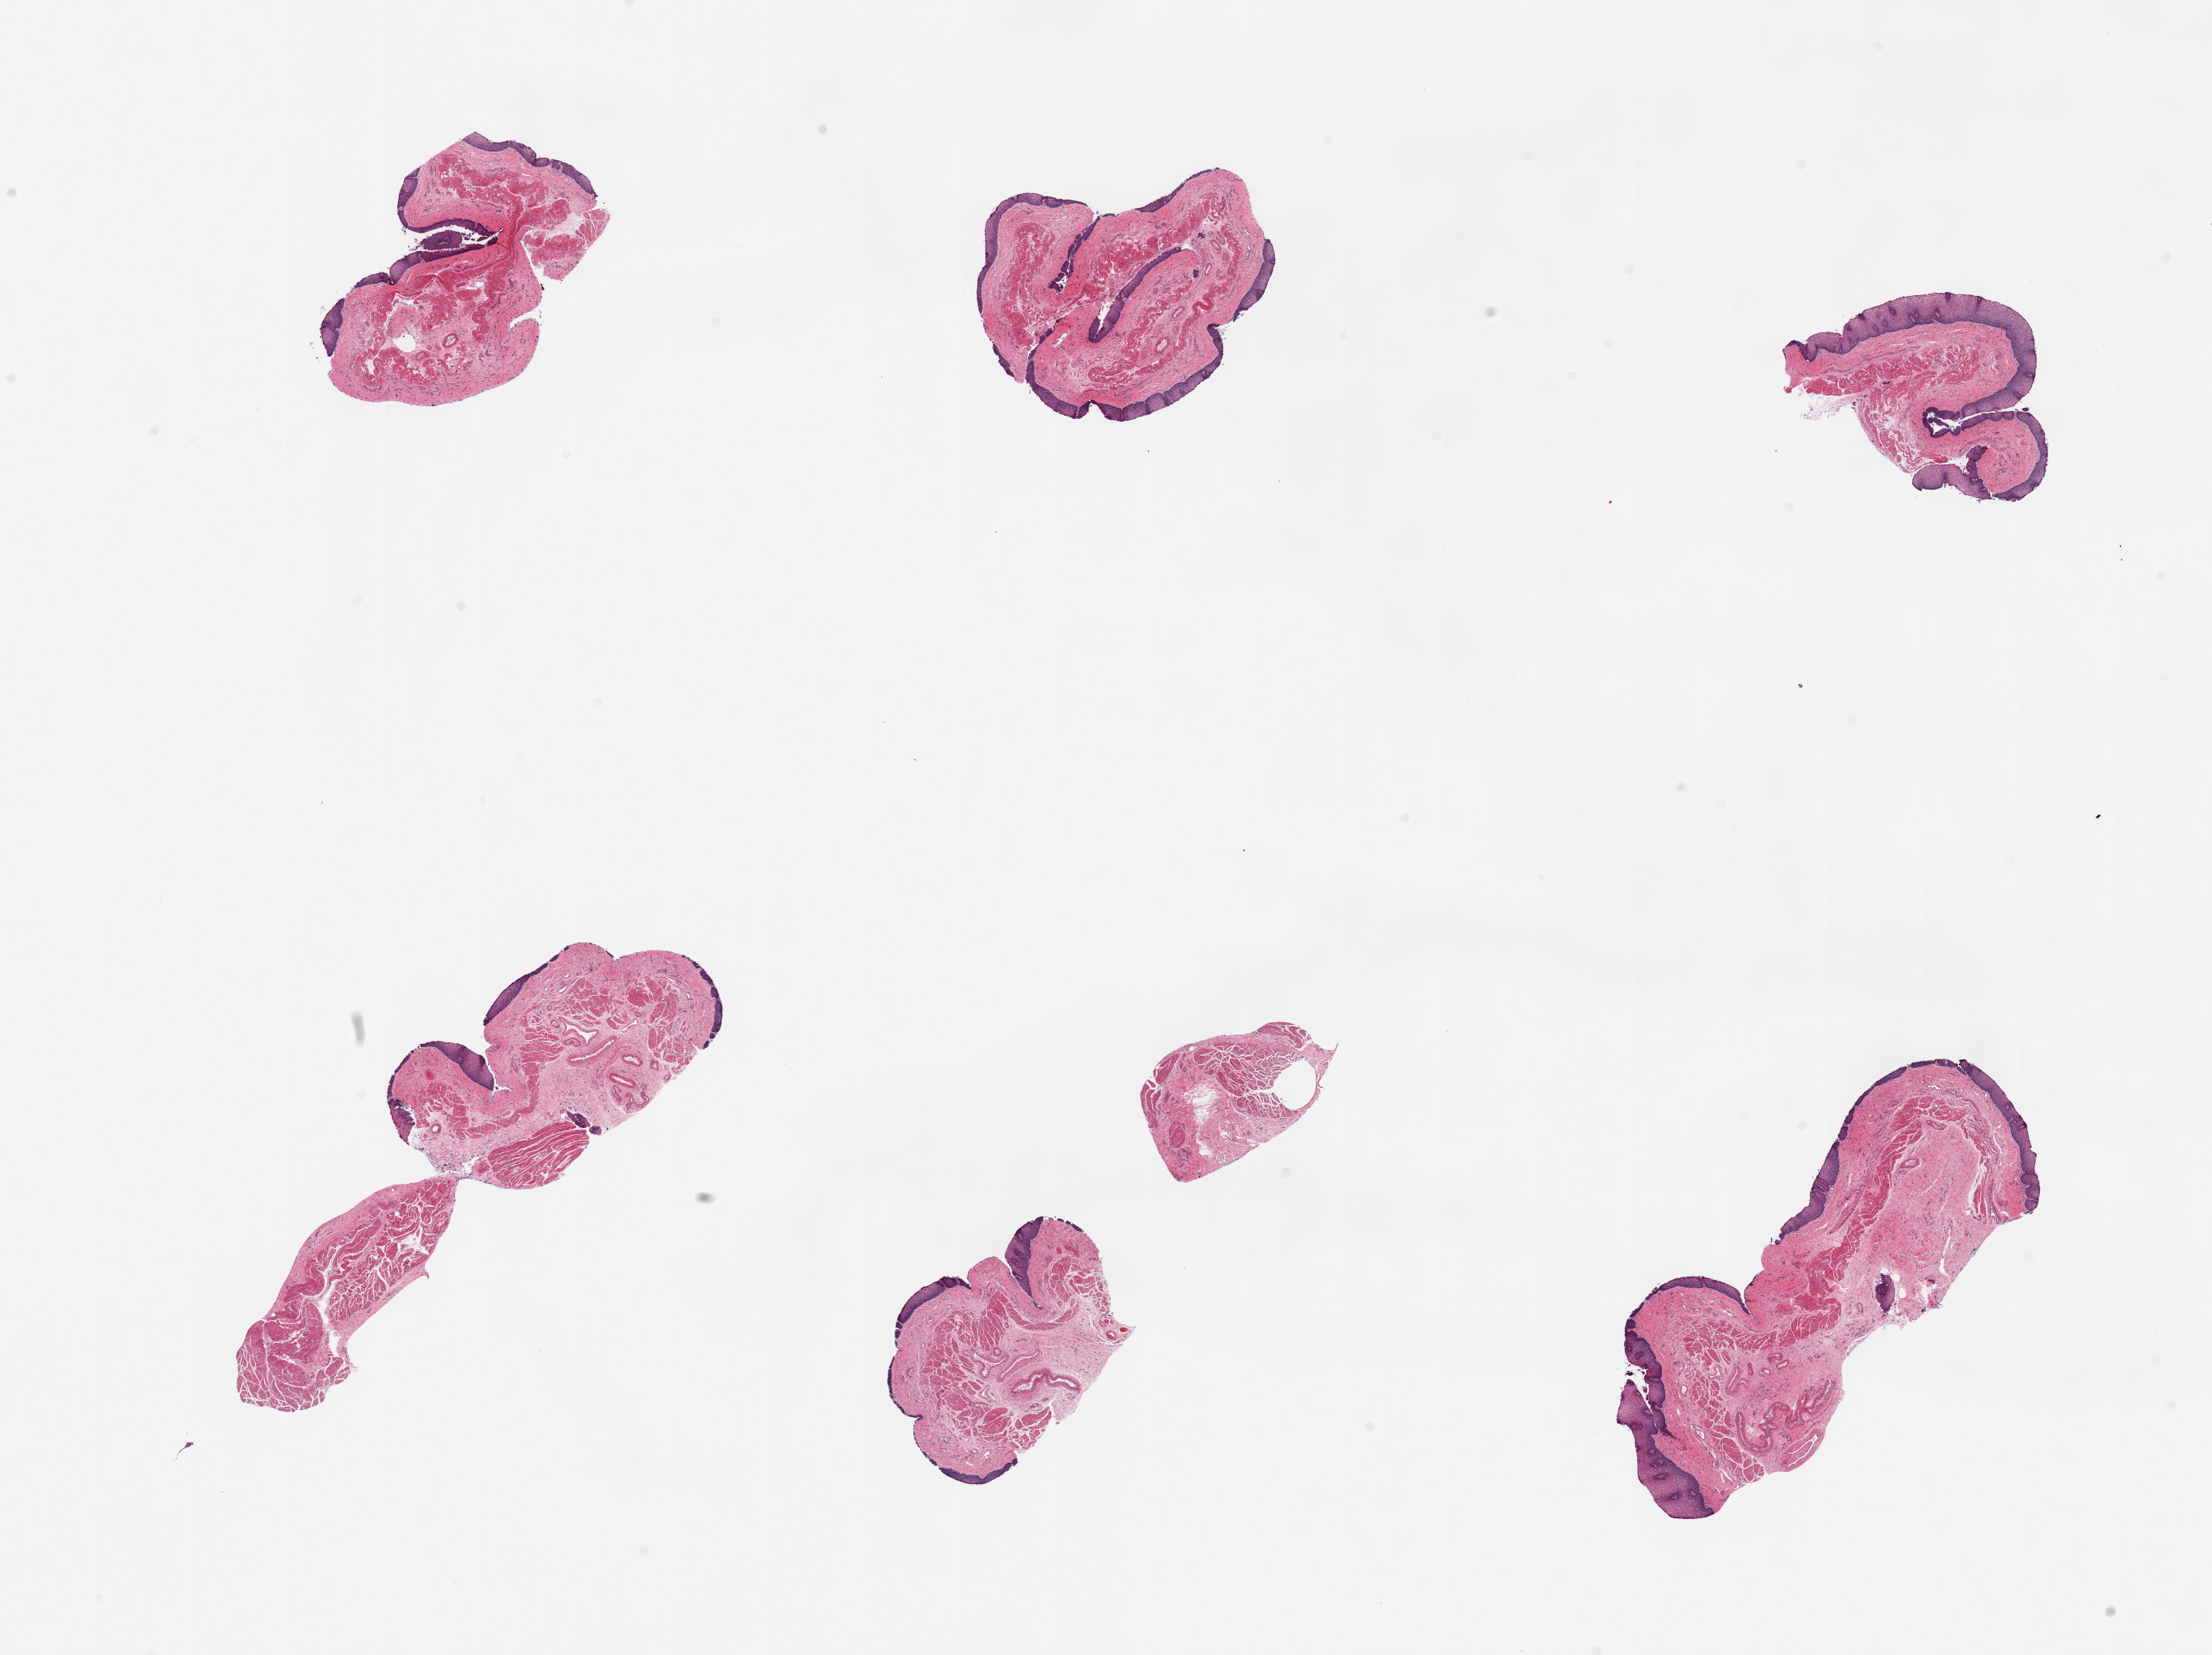
Whole-slide image, haematoxylin and eosin stain, shown as a low-resolution overview of the whole scanned area (about 22.6 x 16.9 mm, acquisition: 20x scan), PAXgene-fixed paraffin-embedded (PFPE) section, section of esophageal mucous membrane (target tissue), donor tissue sample. Female donor.
Pathologist's review note for this sample: 6 pieces; few fragments of muscularis (not target).